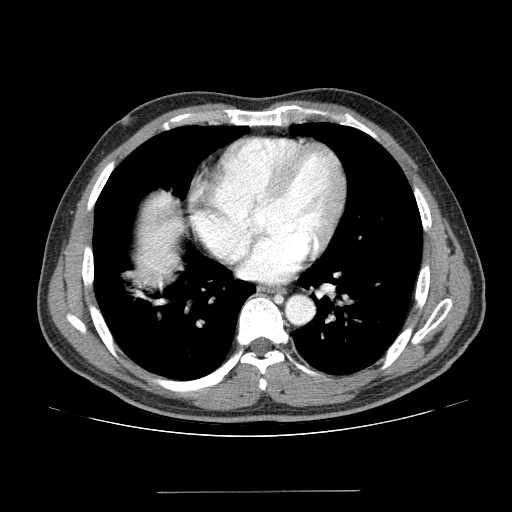
Contrast-enhanced abdominal CT (liver protocol), one axial slice; slice 125 of 131 in the series (ordered by position); reconstruction kernel STANDARD; 100 kVp; one of 2 acquisitions stored at this slice position; soft-tissue window (W 400 / L 40 HU); 512 × 512 image matrix, field of view 380 × 380 mm. From the clinical record (not read from this slice): diagnosis: hepatocellular carcinoma (patient treated with transarterial chemoembolisation; whether this scan precedes or follows treatment is not stated here); TNM stage (as recorded): Stage-I.
Structures marked on this image (semi-automatic segmentation, software-assisted and operator-edited):
- liver parenchyma outside the tumour (the mass and vessels are separate outlines, so this box may not span the whole liver): bounding box (x1, y1, x2, y2) in pixels: (136, 192, 182, 286)
- liver vessels: (160, 201, 166, 285)